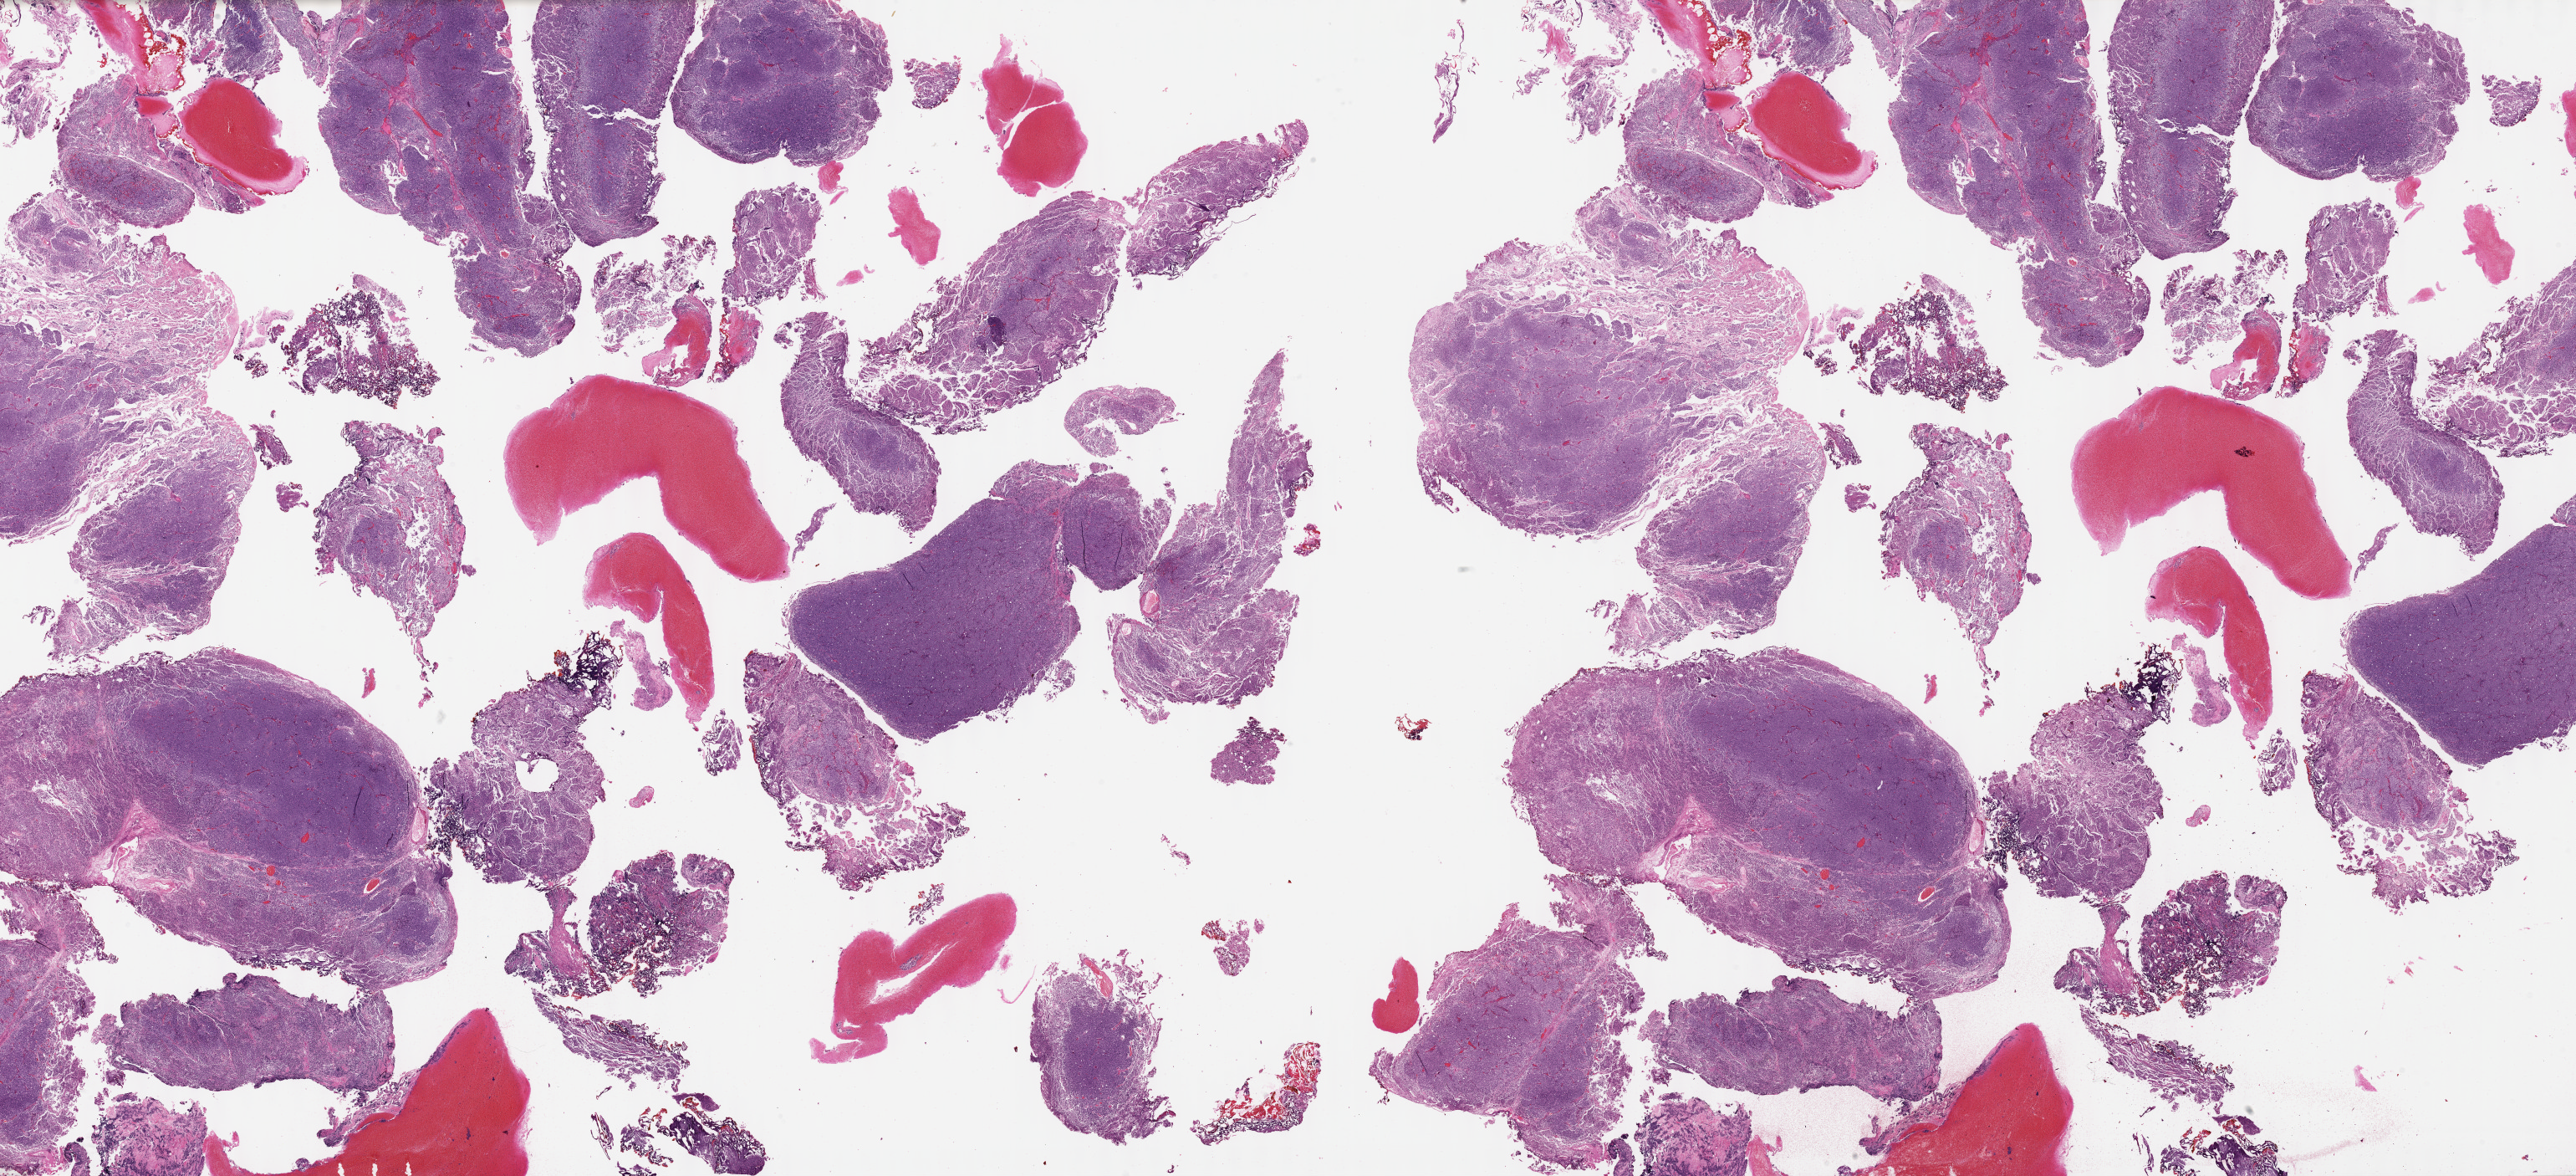
H&E-stained whole-slide image — shown as a low-resolution overview of the whole scanned area (about 49.8 x 22.7 mm), formalin-fixed paraffin-embedded (FFPE) diagnostic section, primary tumour sample from the prostate. Male, age 59 years at initial diagnosis. Gleason score: 10 (5+5).
• diagnosis: Adenocarcinoma, NOS